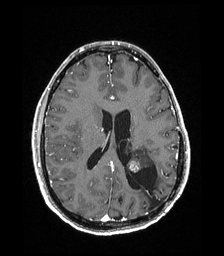
Brain MRI from a brain-tumour surgery series, one axial slice; position 82 of 192 along the scan axis; T1-weighted post-contrast; 1 mm slice thickness; 224 × 256 image matrix, field of view 224 × 256 mm. Case-level facts recorded for this patient, not image findings: histopathology: Low grade glioma; IDH mutation: no.
Outlined on this slice (manually delineated by an expert):
- previous resection cavity: bounding box <126,165,163,208> (left, top, right, bottom; pixels)
- tumour: <127,146,153,173>